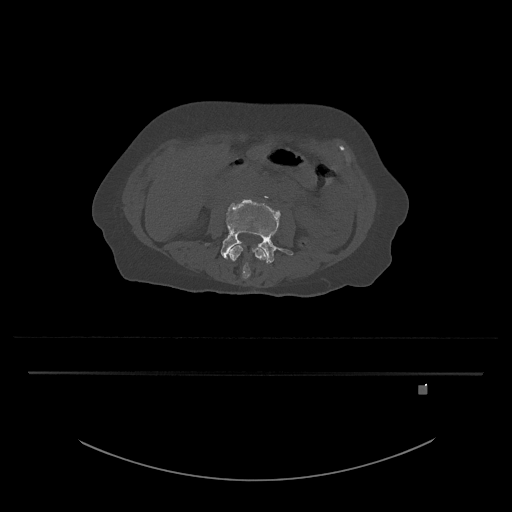
CT including the spine, one axial slice; slice 387 of 797 in the series (ordered by position); reconstruction kernel Br40s/3; 120 kVp; bone window (W 1800 / L 400 HU); 0.5 mm slice thickness; 512 × 512 image matrix, field of view 500 × 500 mm. Patient: female, 57 years. From the clinical record (not read from this slice): primary cancer: cervical.
Annotated regions visible in this slice (semi-automatic segmentation, software-assisted and operator-edited):
- L3 vertebra: bounding box <229,245,268,279> (left, top, right, bottom; pixels)
- L4 vertebra: <206,199,293,264>